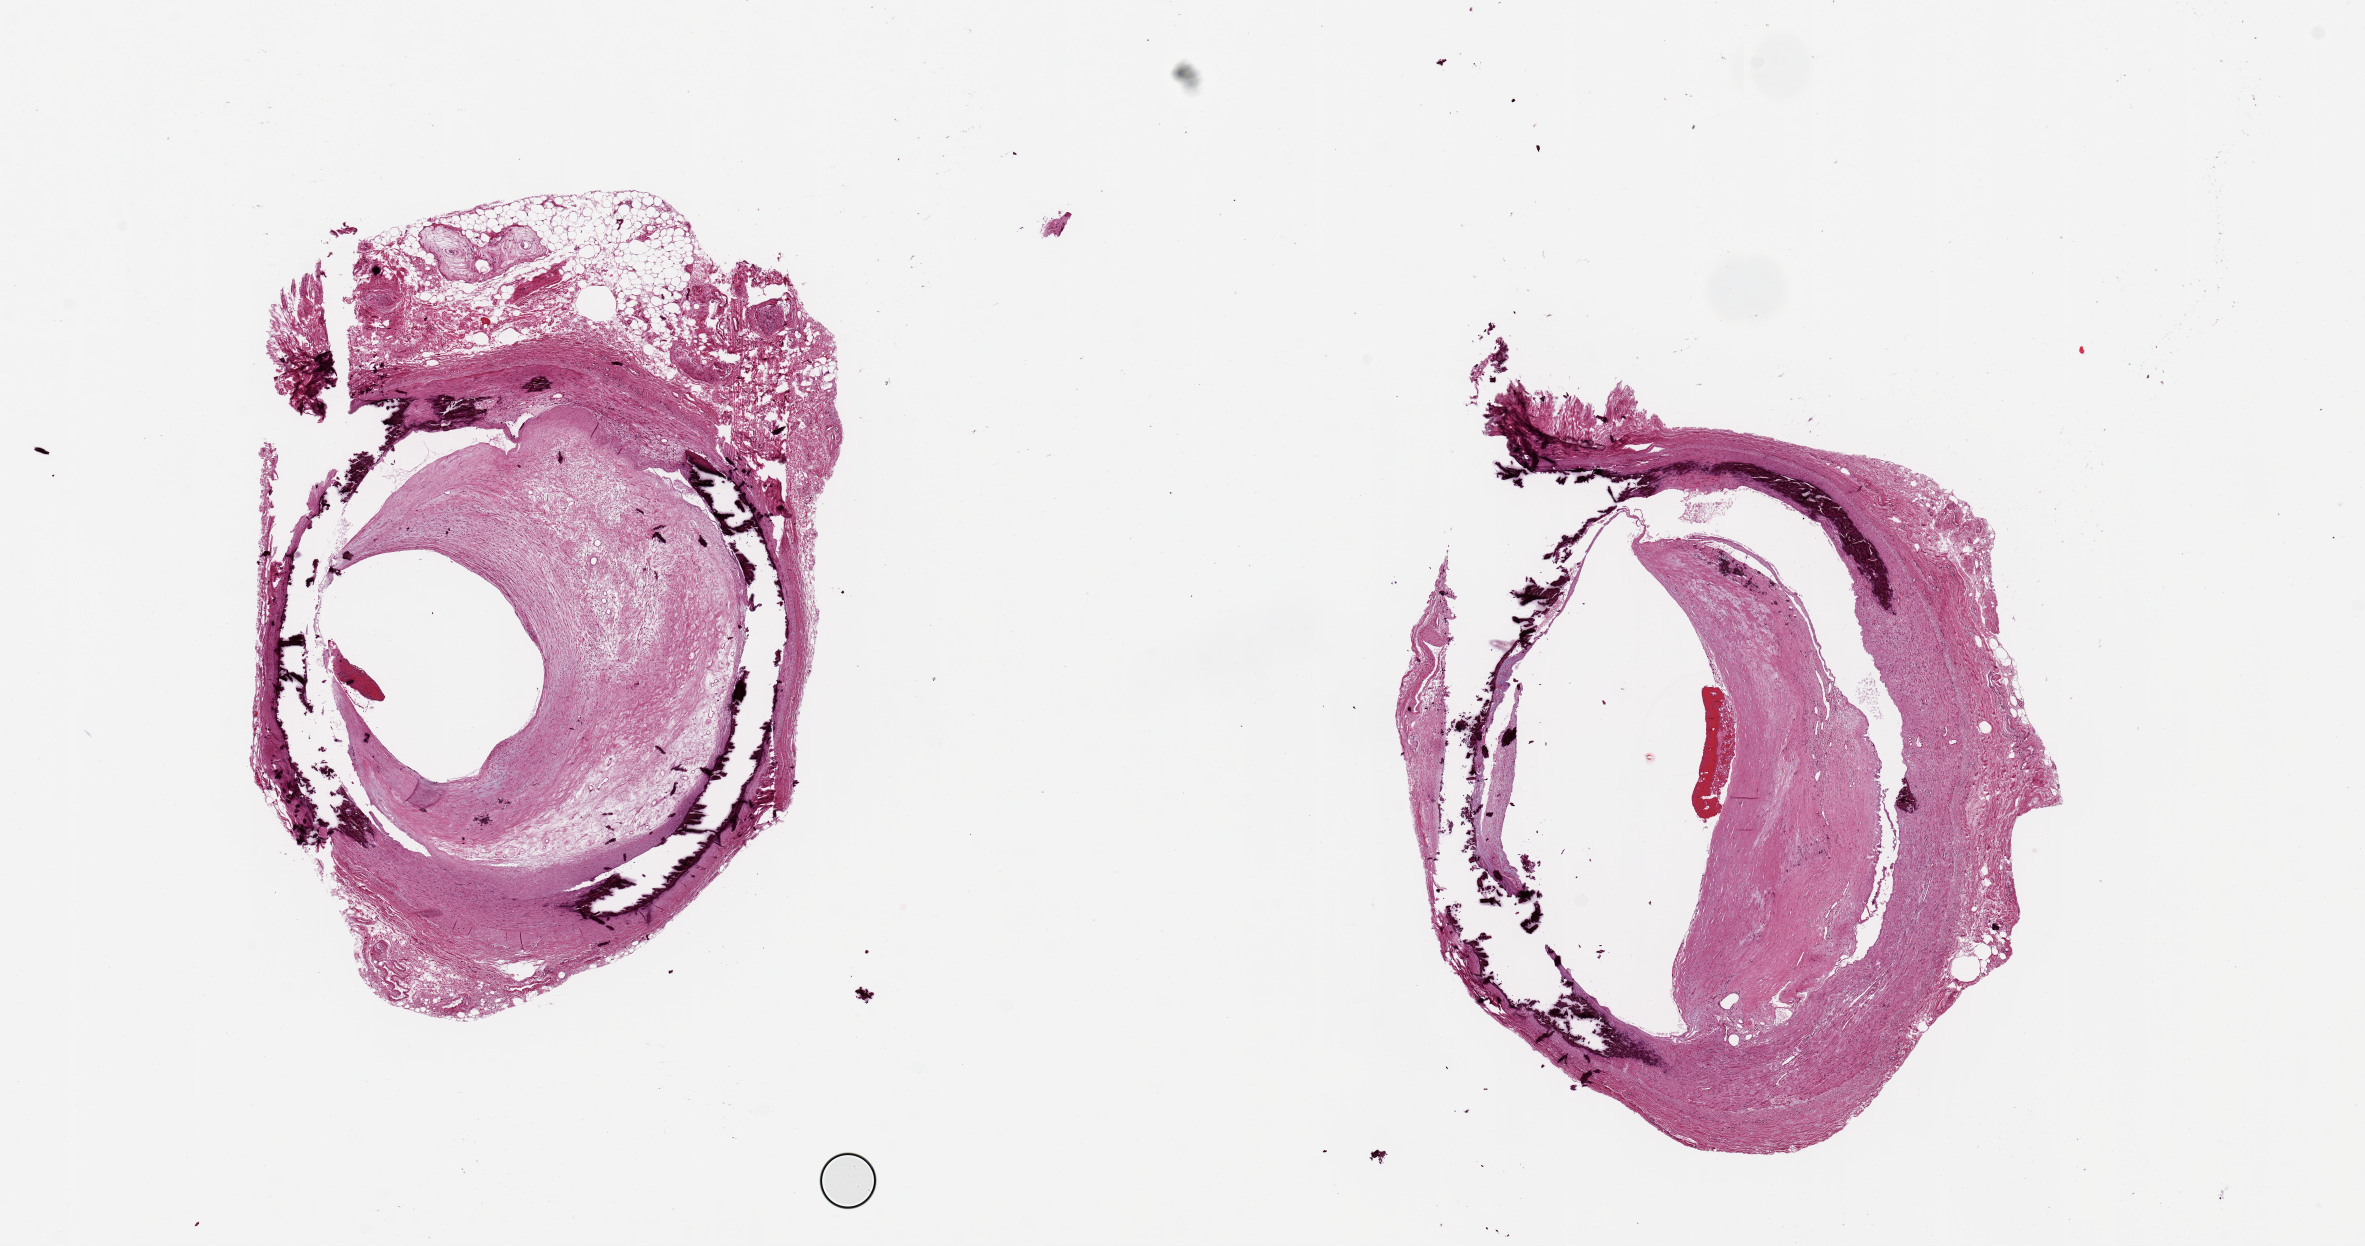
Haematoxylin and eosin whole-slide image, shown as a low-resolution overview of the whole scanned area (about 18.7 x 9.9 mm, acquisition: 20x scan); PAXgene-fixed, paraffin-embedded tissue; sampled site (target tissue): tibial artery; donor tissue sample.
Reviewer comment on this tissue sample: 2 ~4.5mm d. aliquots, subtotally occlusive & calcifying atherosclerotic luminal deposits; Monckeberg???s sclerosis of media, extensive.